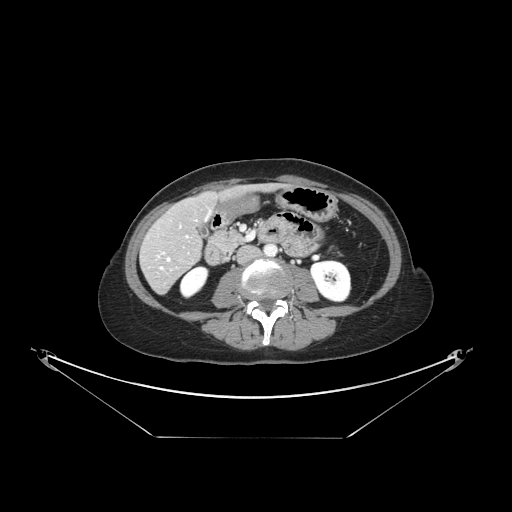
Contrast-enhanced abdominal CT, one axial slice; slice 46 of 148 in the series (ordered by position); reconstruction kernel STANDARD; 120 kVp; intravenous contrast given; soft-tissue window (W 400 / L 40 HU); 2.5 mm slice thickness; 512 × 512 image matrix, field of view 500 × 500 mm. Female patient, age 73 years. Case-level facts recorded for this patient, not image findings: diagnosis: colorectal cancer liver metastases, imaged before liver resection; multiple liver metastases: no; largest metastasis: 1 cm.
Outlined on this slice (manually delineated by an expert):
- hepatic veins: bounding box <158,226,188,269> (left, top, right, bottom; pixels)
- liver: <143,194,217,293>
- planned liver remnant (the part of the liver to remain after resection): <161,194,217,243>